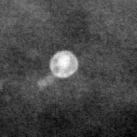
Cropped region of a digitized screen-film mammogram centred on a radiologist-marked abnormality; left breast; CC view.
Finding: calcifications, morphology round and regular / lucent center / punctate, distribution diffusely scattered; BI-RADS assessment category 2; subtlety rating 5 on a 1 (subtle) to 5 (obvious) scale; benign; no additional work-up was recommended (benign without callback).